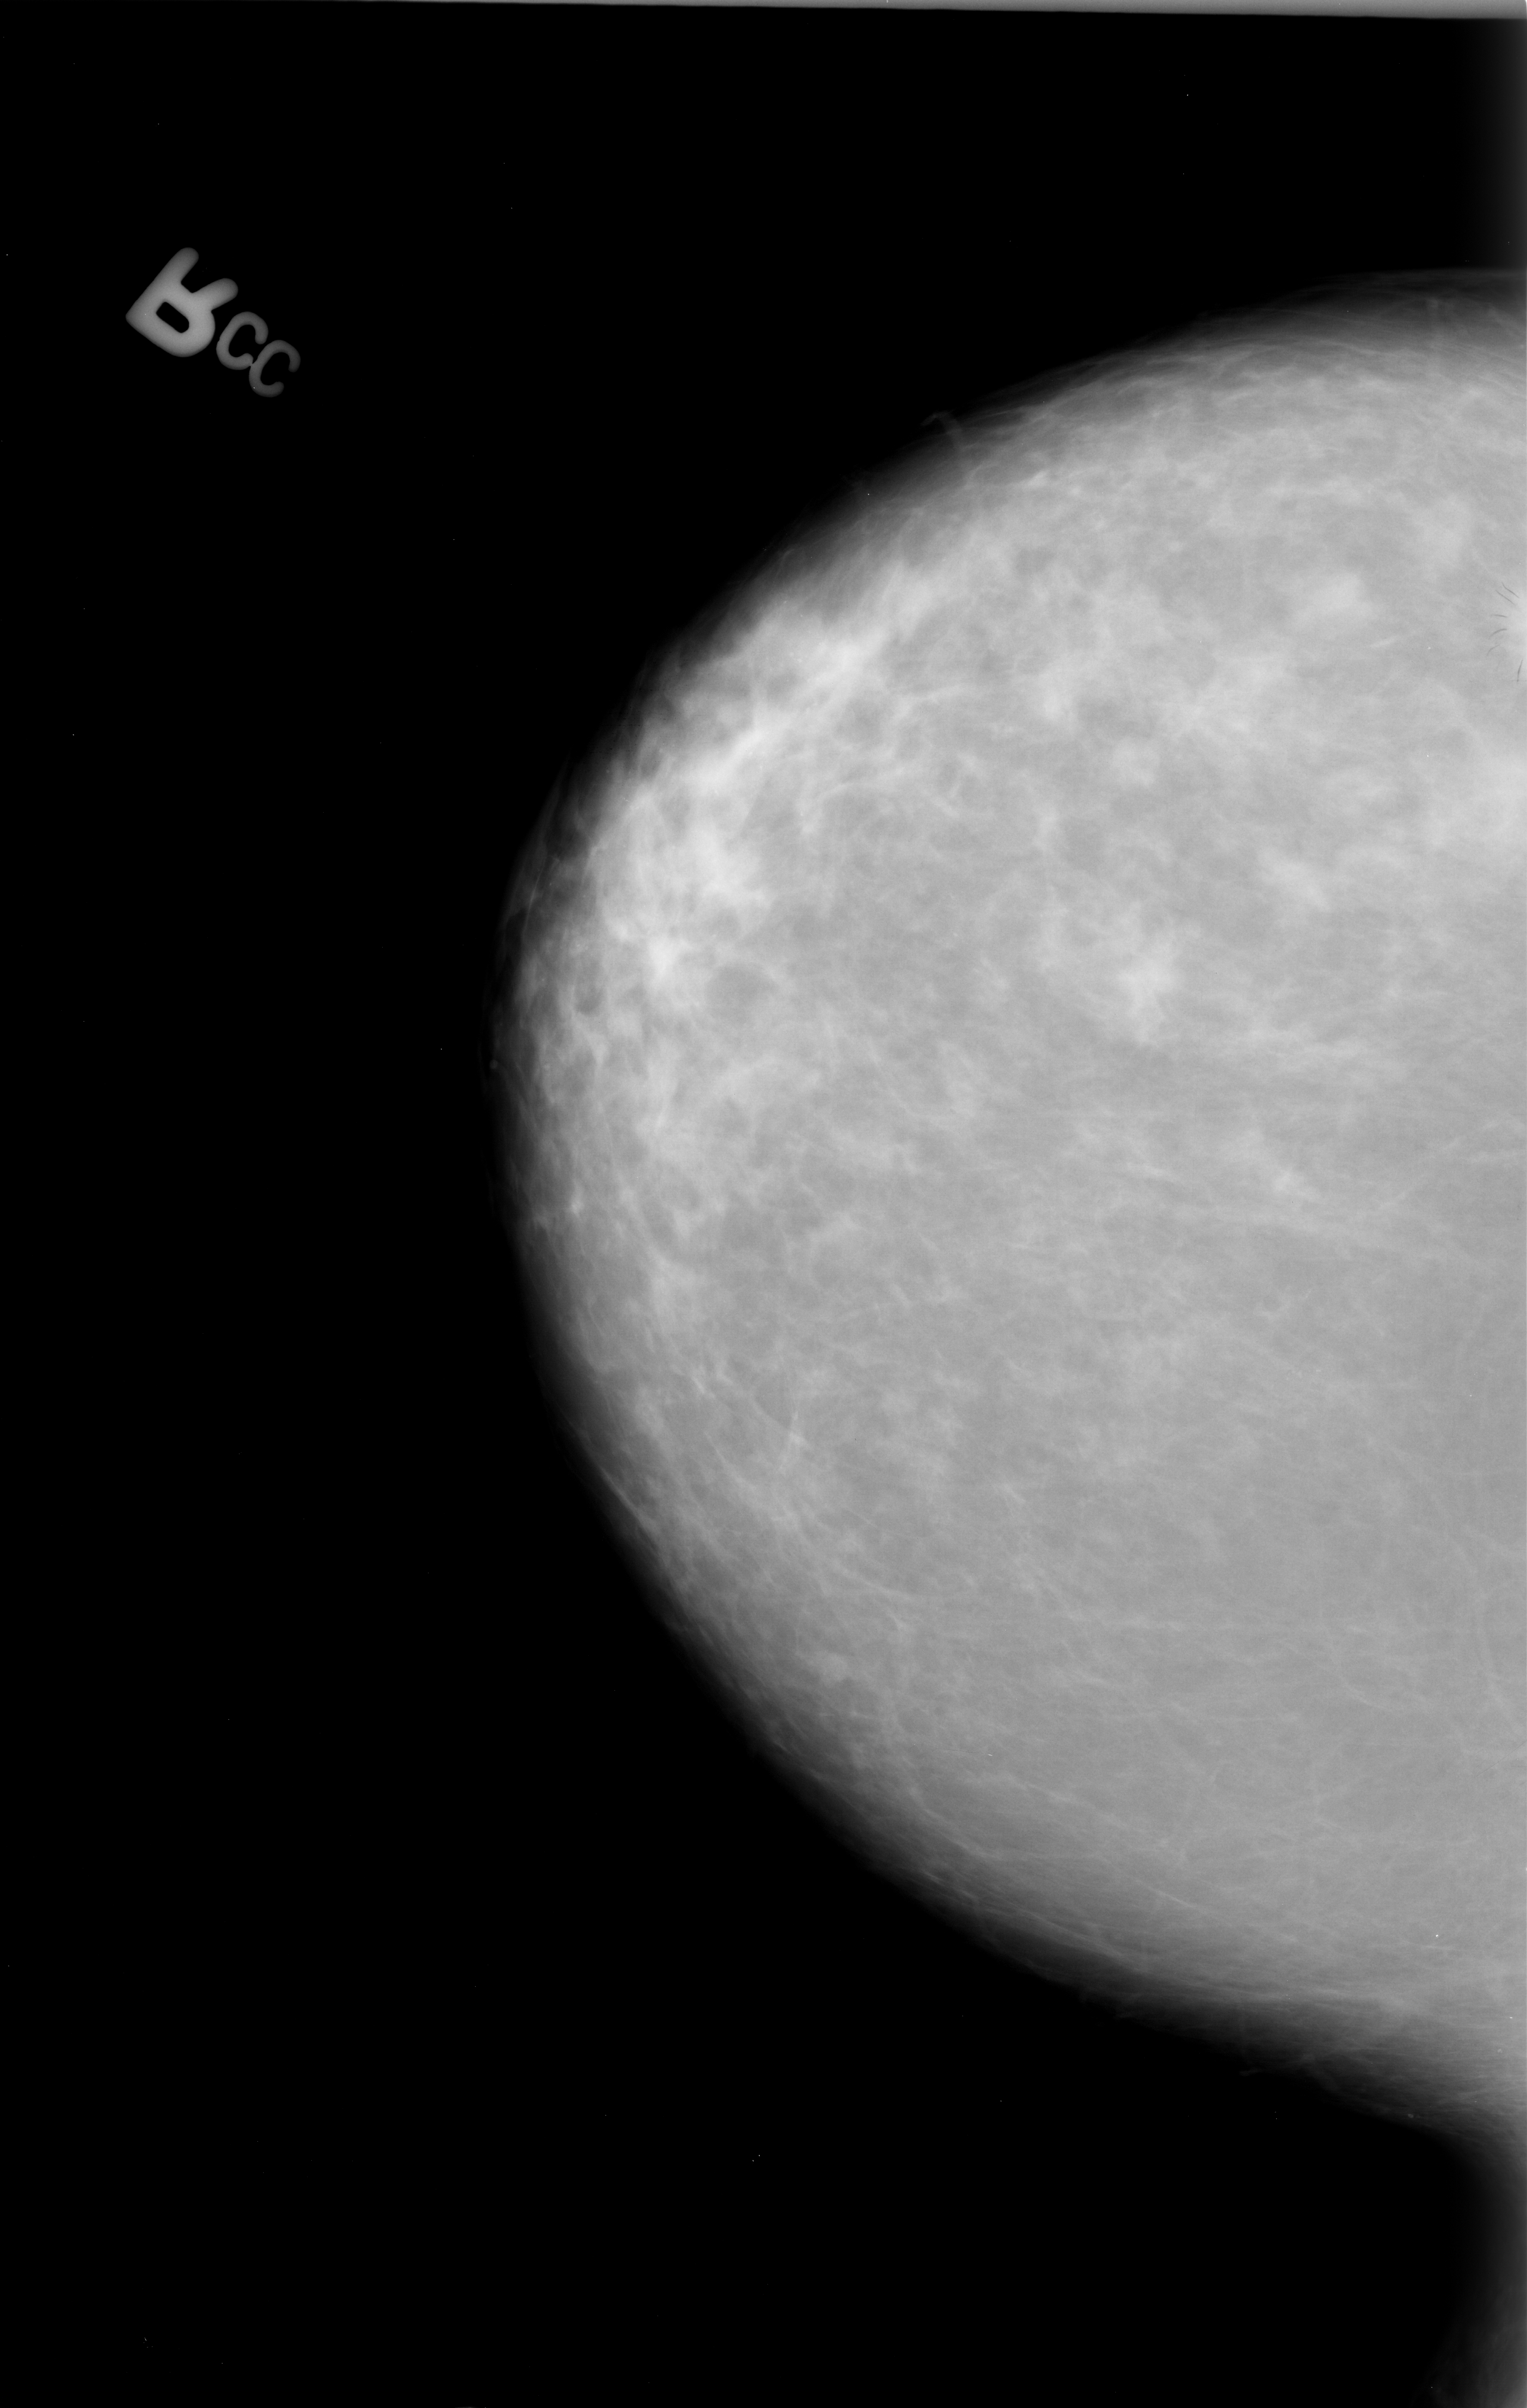
Mammogram (digitized film). Right breast. CC view. Breast composition: scattered fibroglandular densities (BI-RADS density category 2 of 4). 1527 × 2408 image matrix.
Expert-marked regions of interest on this image (one box per marked abnormality):
- mass, shape architectural distortion, margins spiculated; BI-RADS assessment category 4; pathology (as recorded): malignant: bounding box <1471,570,1527,681> (left, top, right, bottom; pixels)